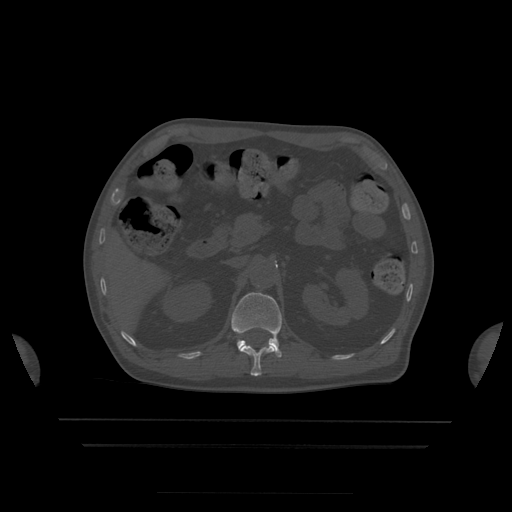
CT including the spine, one axial slice; slice 182 of 522 in the series (ordered by position); bone window (W 1800 / L 400 HU); 1.25 mm slice thickness; 512 × 512 image matrix. Patient age 68 years. Case-level facts recorded for this patient, not image findings: primary cancer: urothelial.
Outlined on this slice (semi-automatic segmentation, software-assisted and operator-edited):
- L1 vertebra: bounding box [x1, y1, x2, y2] px = [232, 293, 282, 358]
- T12 vertebra: [241, 345, 275, 376]